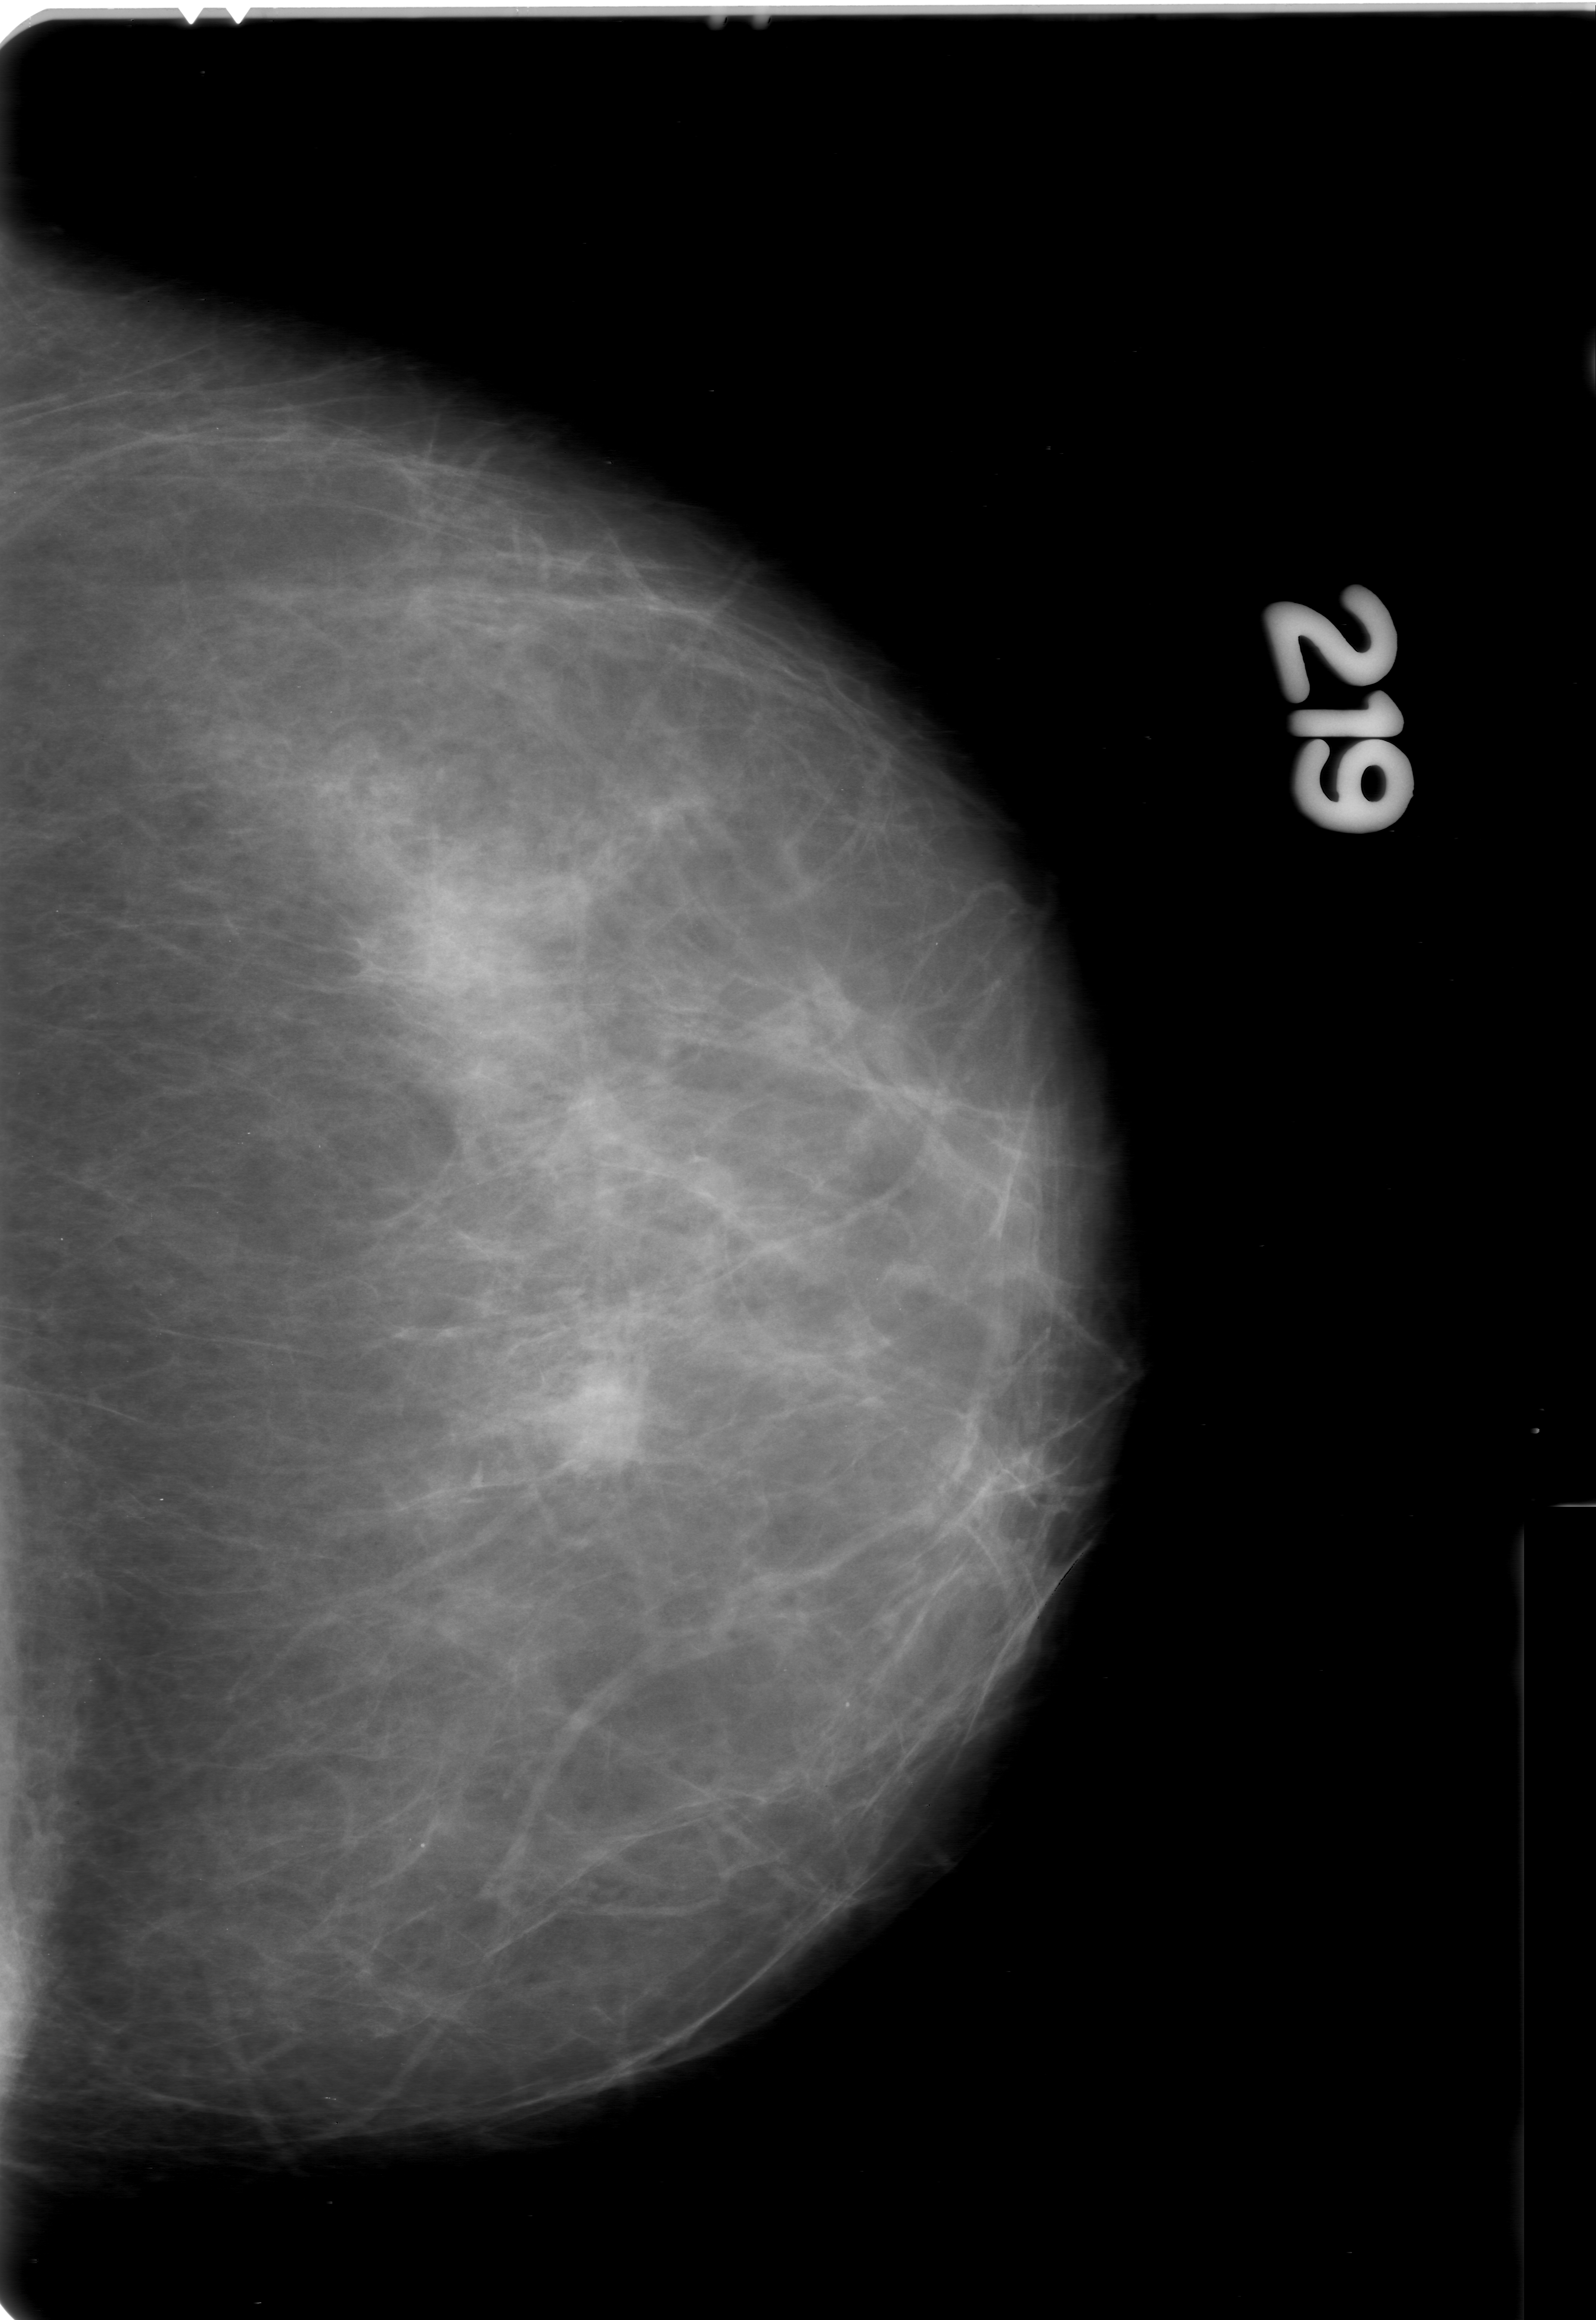
Scanned film-screen mammogram; left breast; CC view; BI-RADS breast density category 2 (scale 1–4); 1596 × 2320 image matrix.
Expert-marked regions of interest on this image (one box per marked abnormality):
- mass, shape oval, margins obscured; BI-RADS assessment category 4; subtlety rating 4 on a 1 (subtle) to 5 (obvious) scale; pathology result (as recorded, not read from the image): malignant: box from (x=513, y=1356) to (x=666, y=1490) px